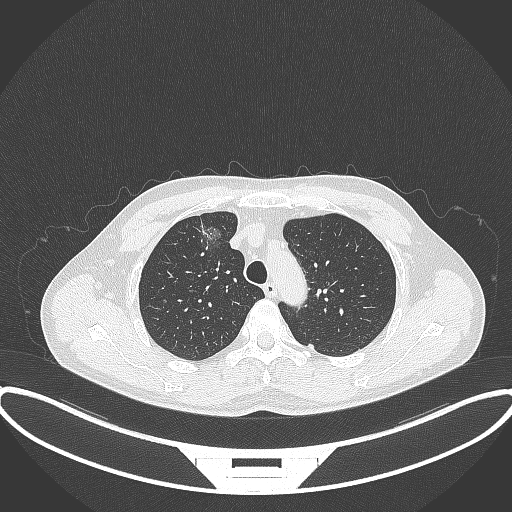
Chest CT, one axial slice; position 282 of 395 along the scan axis; reconstruction kernel B70f; 120 kVp; lung window (W 1500 / L -600 HU); 1 mm slice thickness; 512 × 512 image matrix, field of view 424 × 424 mm. Patient: male, 60 years. Case-level facts recorded for this patient, not image findings: clinical TNM (as recorded): T1c N0 M0.
Outlined on this slice (rectangle marked by the reading radiologist):
- lung tumour (recorded histology: adenocarcinoma): bounding box [x1, y1, x2, y2] px = [198, 218, 230, 256]